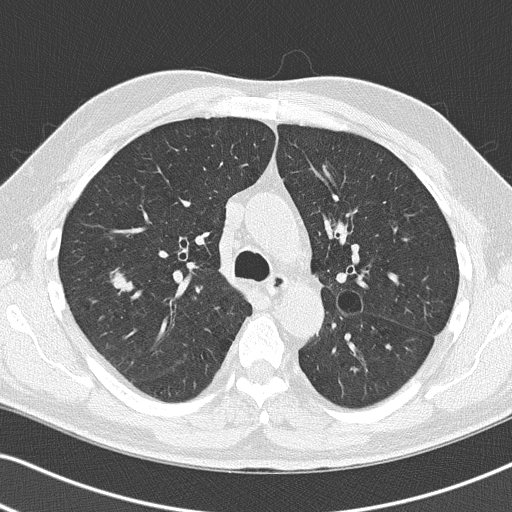
Low-dose screening chest CT, axial slice, first (baseline) screen, lung window (W 1500 / L -600 HU), slice 52 of 140 in the series, 512 × 512 image matrix. Male, age 67 years at enrolment. Former smoker at enrolment.
Lesion marked by an expert reader, bounding box (x1, y1, x2, y2) in pixels: (74, 256, 152, 315). Screening reader's record for this exam (one nodule recorded; not confirmed to be the boxed lesion): non-calcified nodule or mass ≥4 mm, right upper lobe, 26 × 24 mm, spiculated (stellate) margins, soft tissue attenuation. Official screen result: positive, change unspecified: nodule(s) >= 4 mm or enlarging nodule(s), mass(es), or other non-specific abnormalities suspicious for lung cancer. Lung cancer was diagnosed 49 days after this screen: squamous cell carcinoma, NOS, right upper lobe, poorly differentiated (G3), stage IA (AJCC 6th edition), 27 mm at pathology.